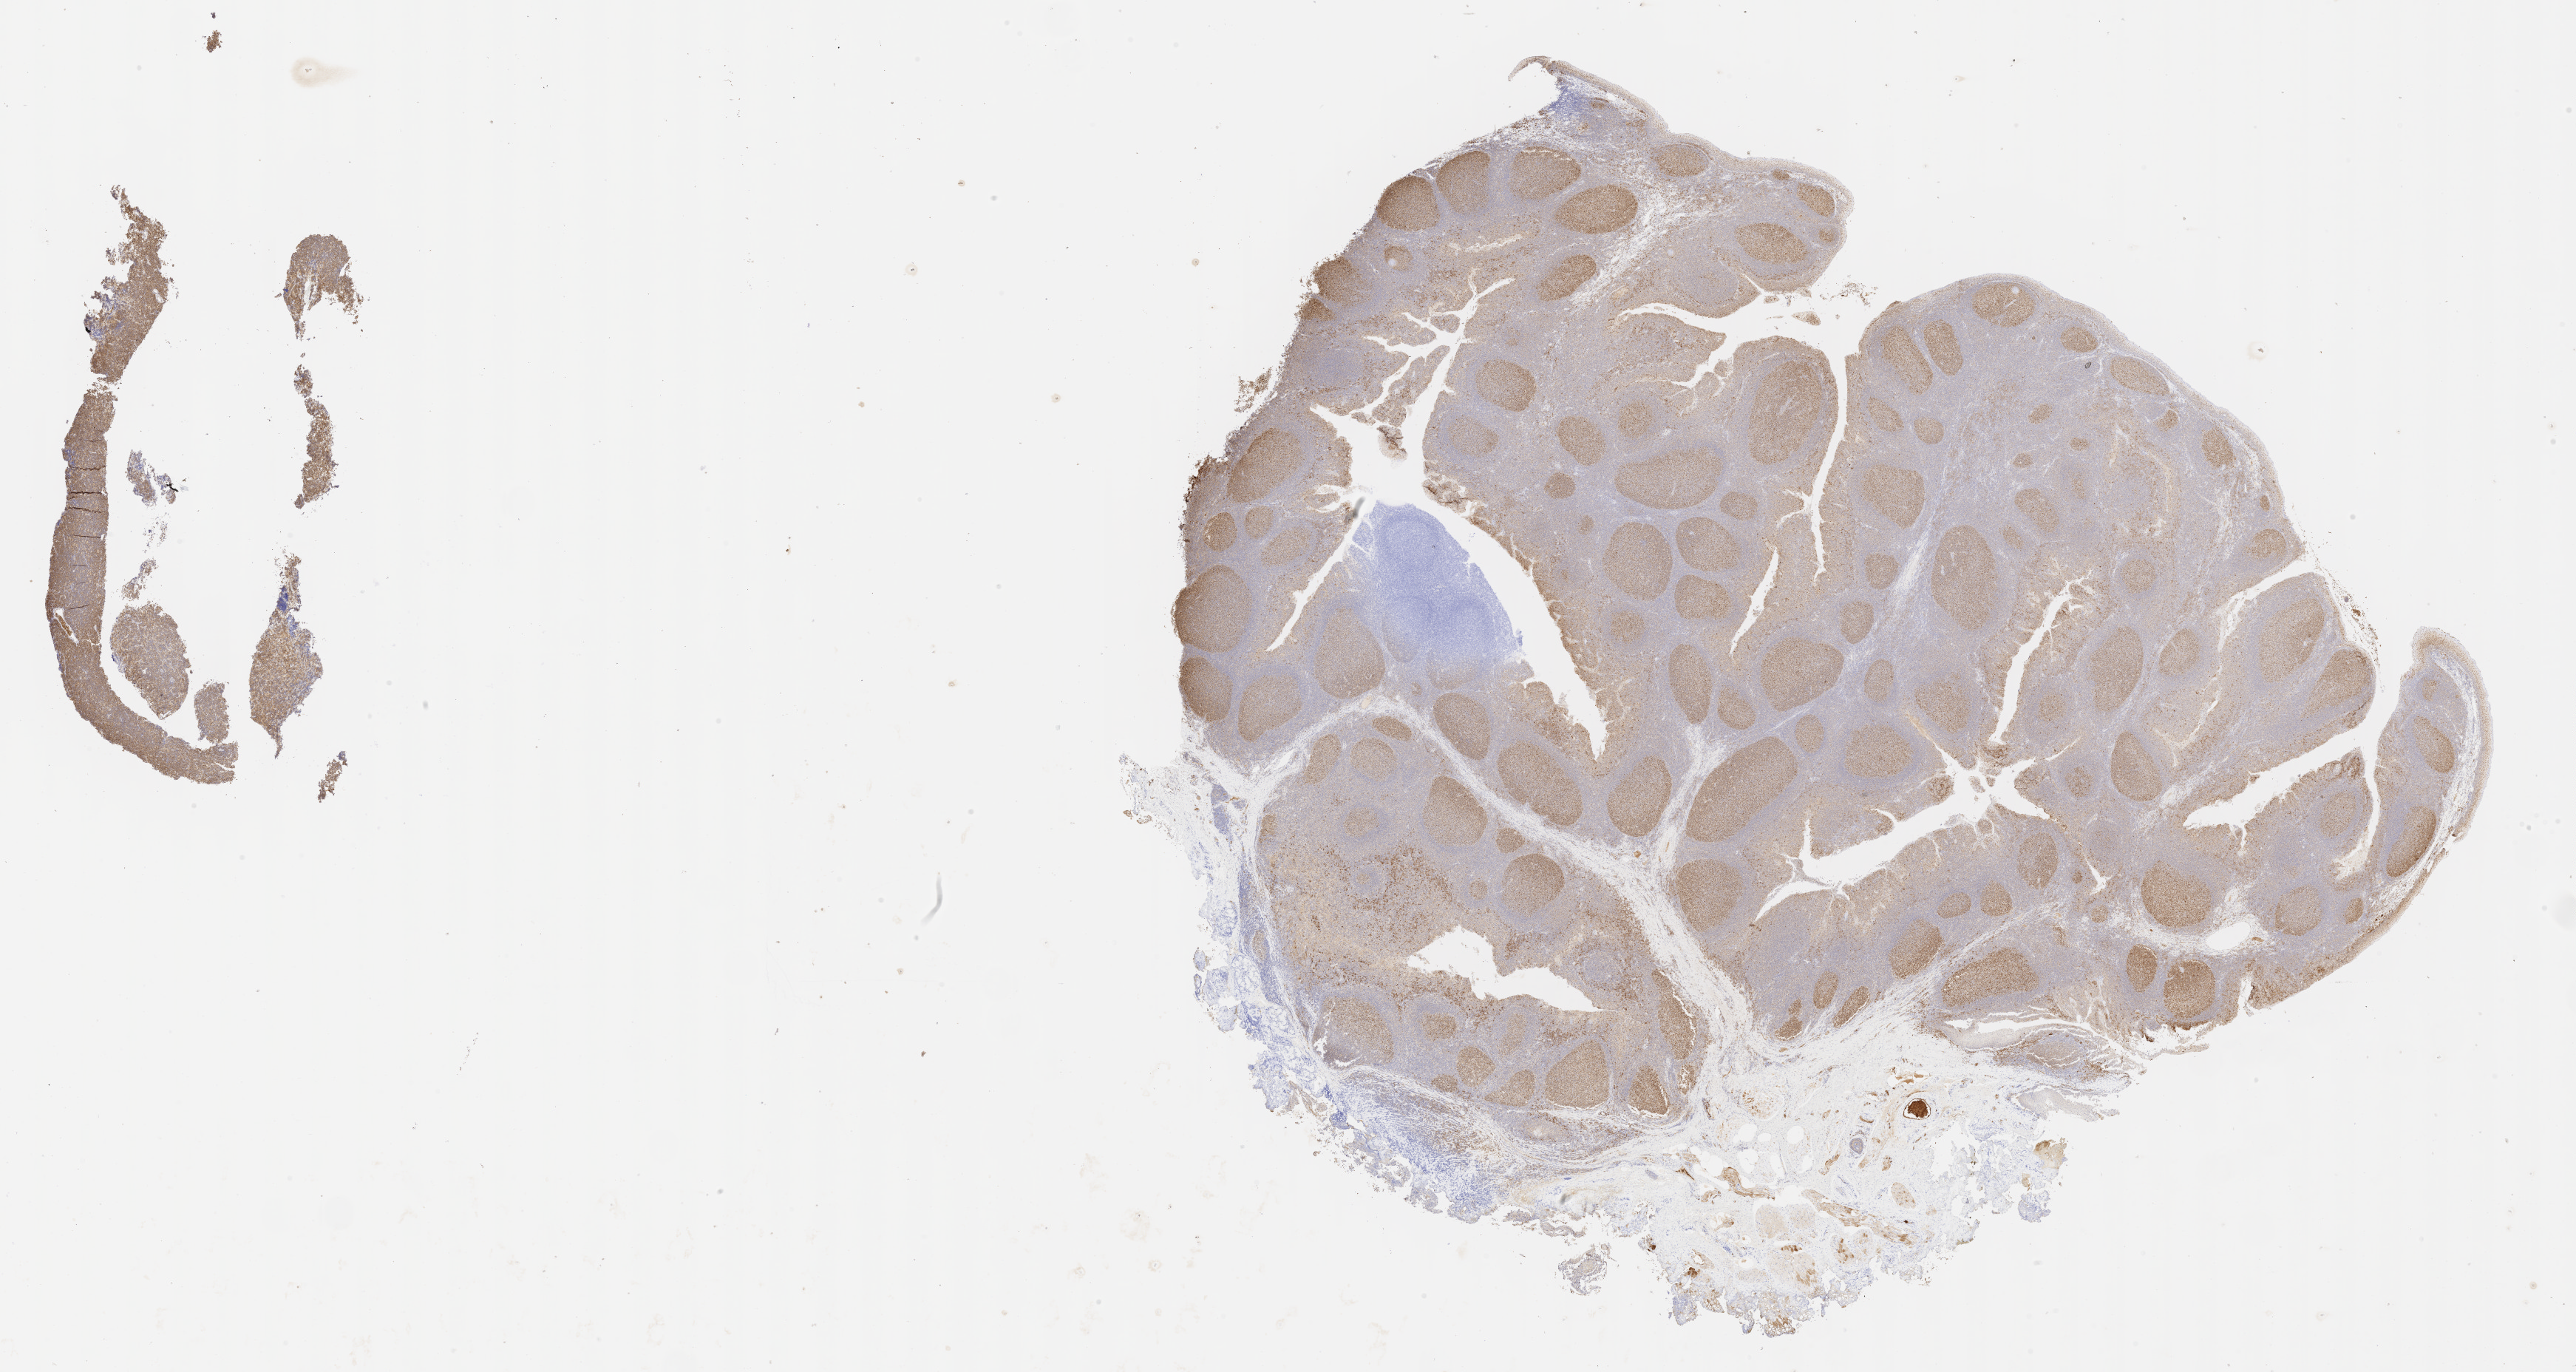
IHC for BCL6, whole-slide image — low-resolution overview of the scanned area, about 28.2 x 15.0 mm. Tumor tissue. Female patient, 10 years old.
Histologic diagnosis: Burkitt lymphoma, NOS.